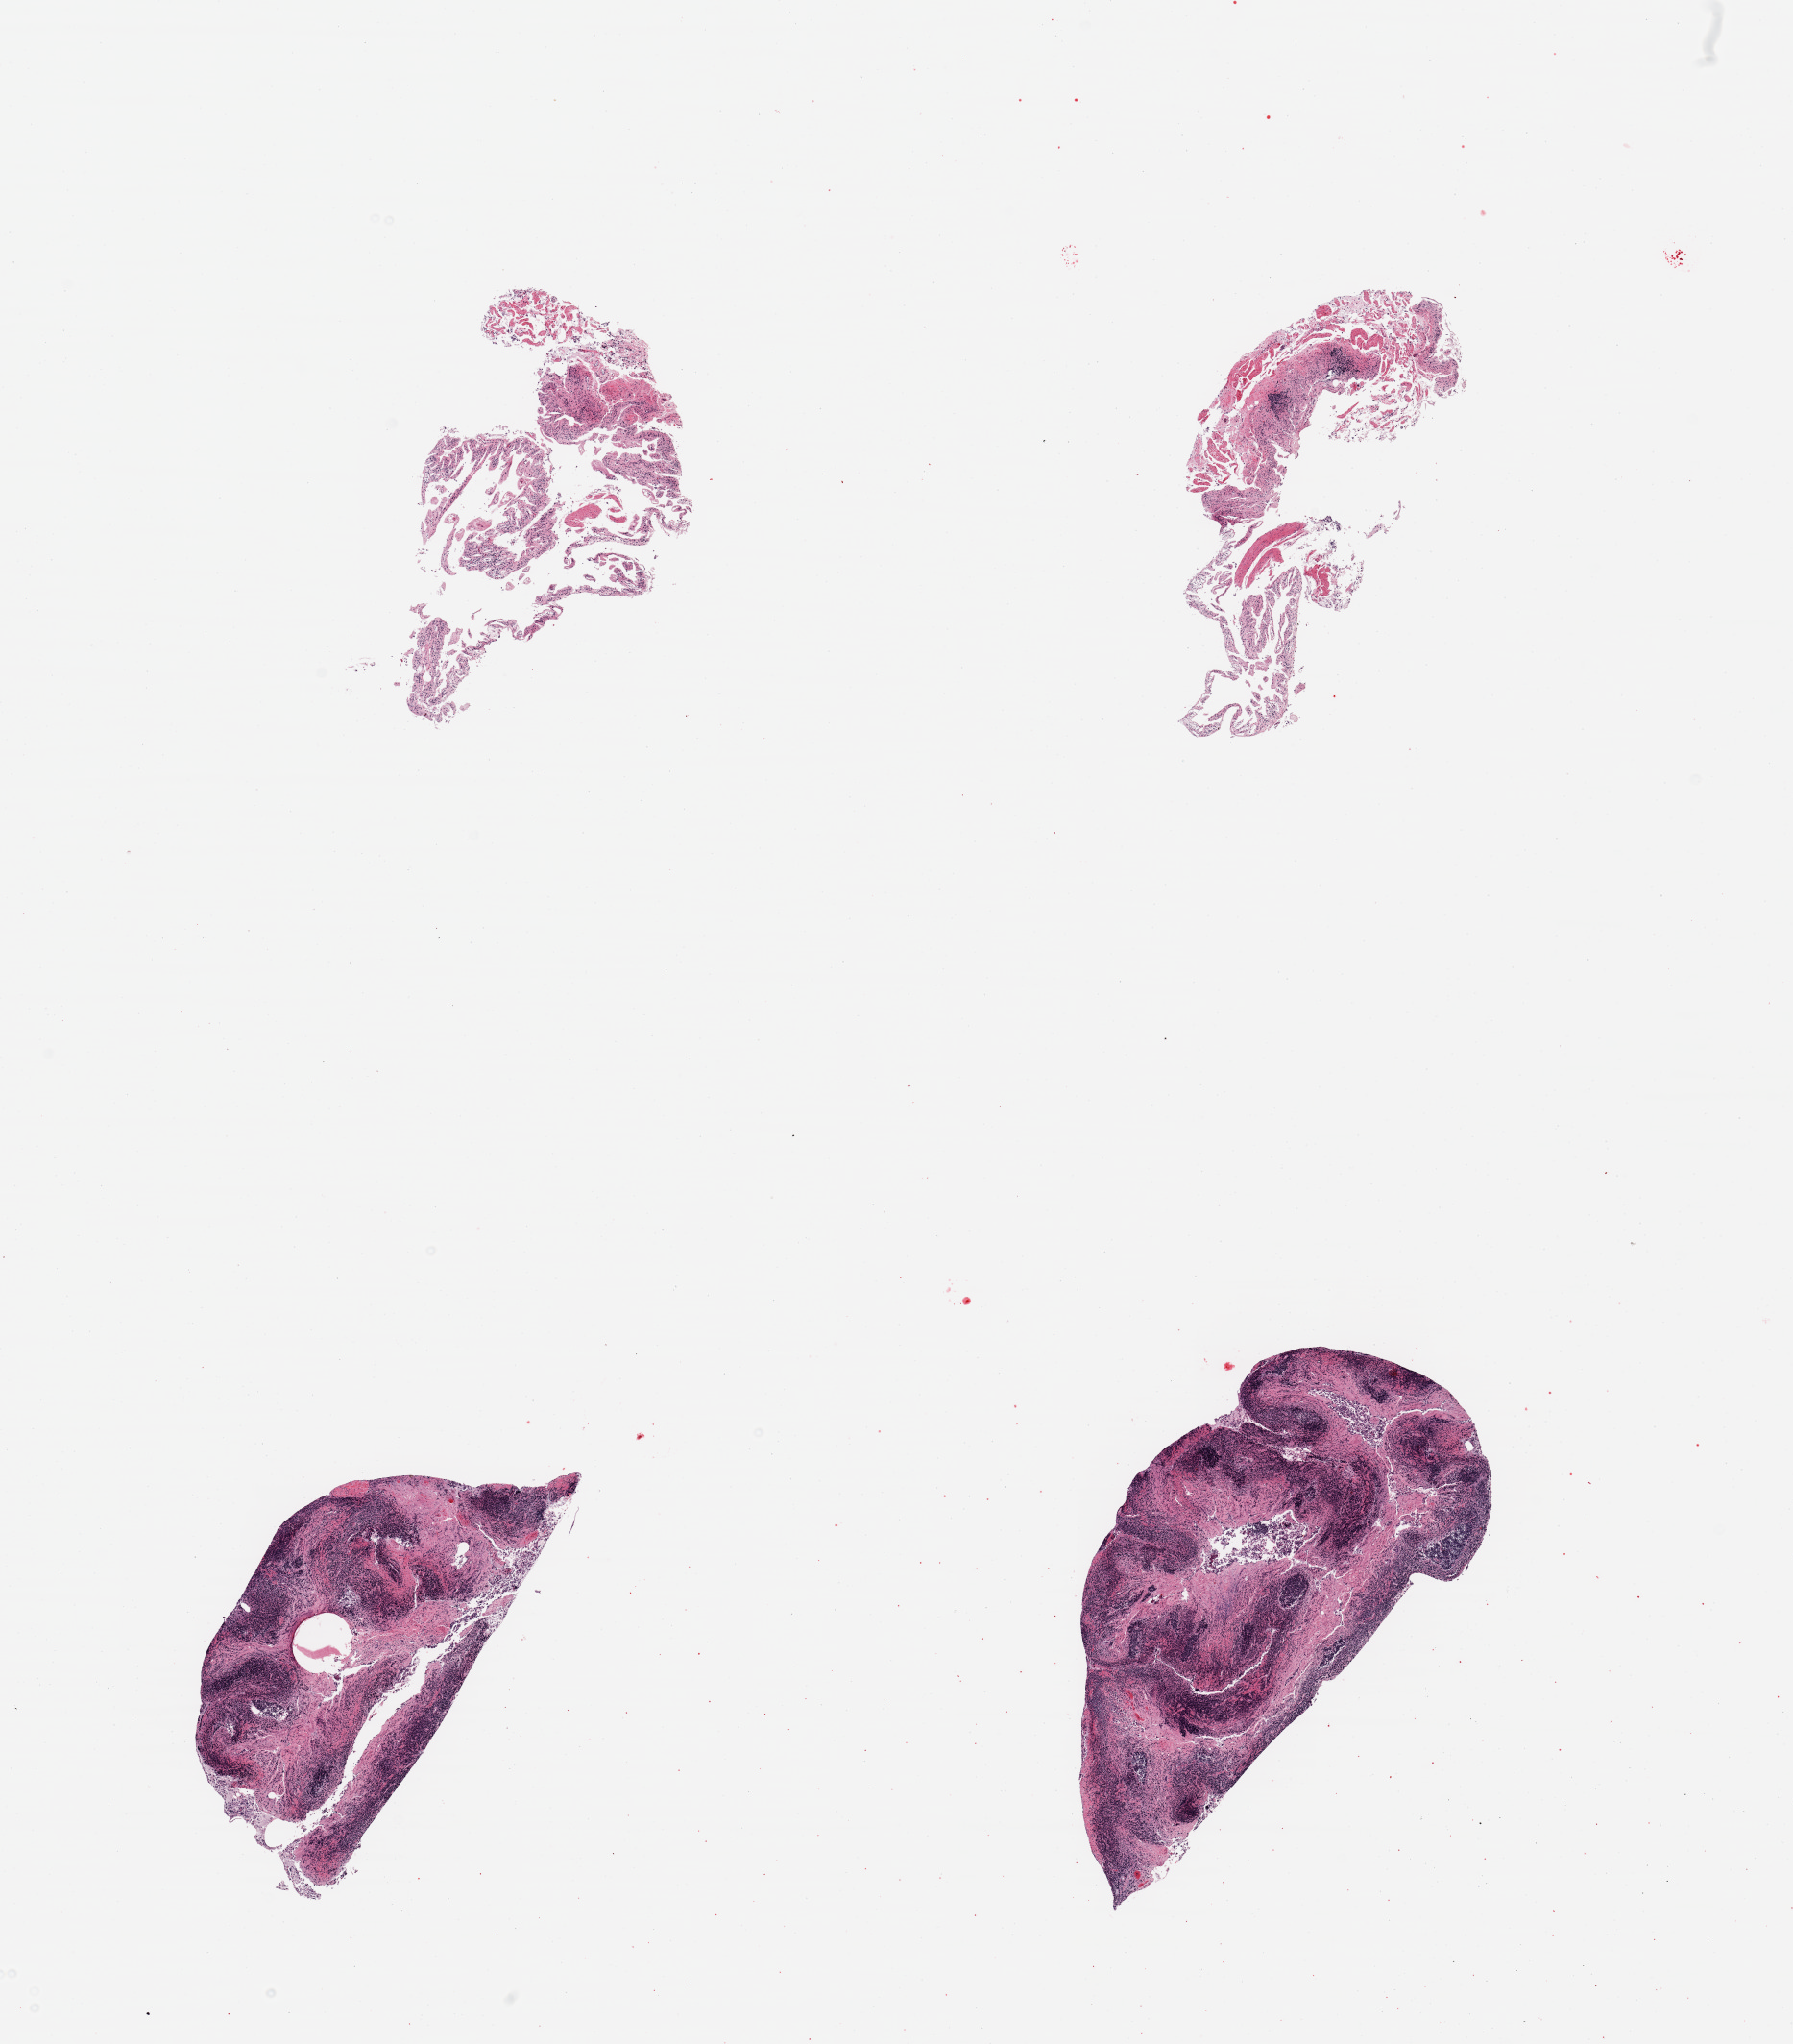
Whole-slide image, hematoxylin and eosin (H&E) stain — whole scanned area (about 14.8 x 16.8 mm, acquisition: 20x scan) shown as a low-resolution overview; PAXgene-fixed paraffin-embedded (PFPE) section; sampled site (target tissue): ileum; tissue donor sample. Donor: male.
Reviewer comment on this tissue sample: 4 pieces; 2 (larger) pieces have much lymphoid tissue, moderately autolyzed; 2 smaller pieces are without significant lymphoid tissue.